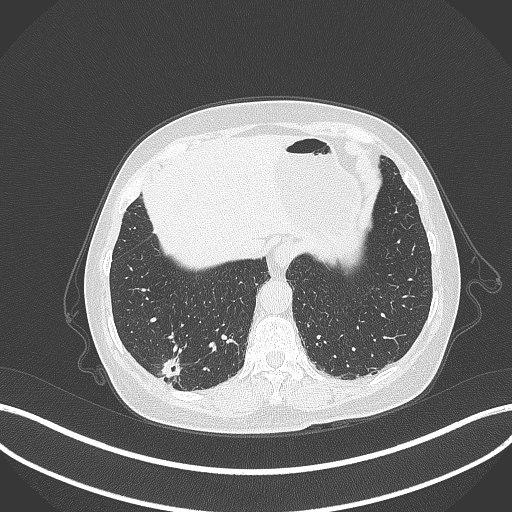
Chest CT, one axial slice; position 55 of 333 along the scan axis; 120 kVp; lung window (W 1500 / L -600 HU); 512 × 512 image matrix, field of view 400 × 400 mm. Female patient, age 69 years. From the clinical record (not read from this slice): clinical TNM (as recorded): T1b N0 M0.
Annotated regions visible in this slice (rectangle marked by the reading radiologist):
- lung tumour (recorded histology: adenocarcinoma): bounding box [x1, y1, x2, y2] px = [157, 351, 188, 385]